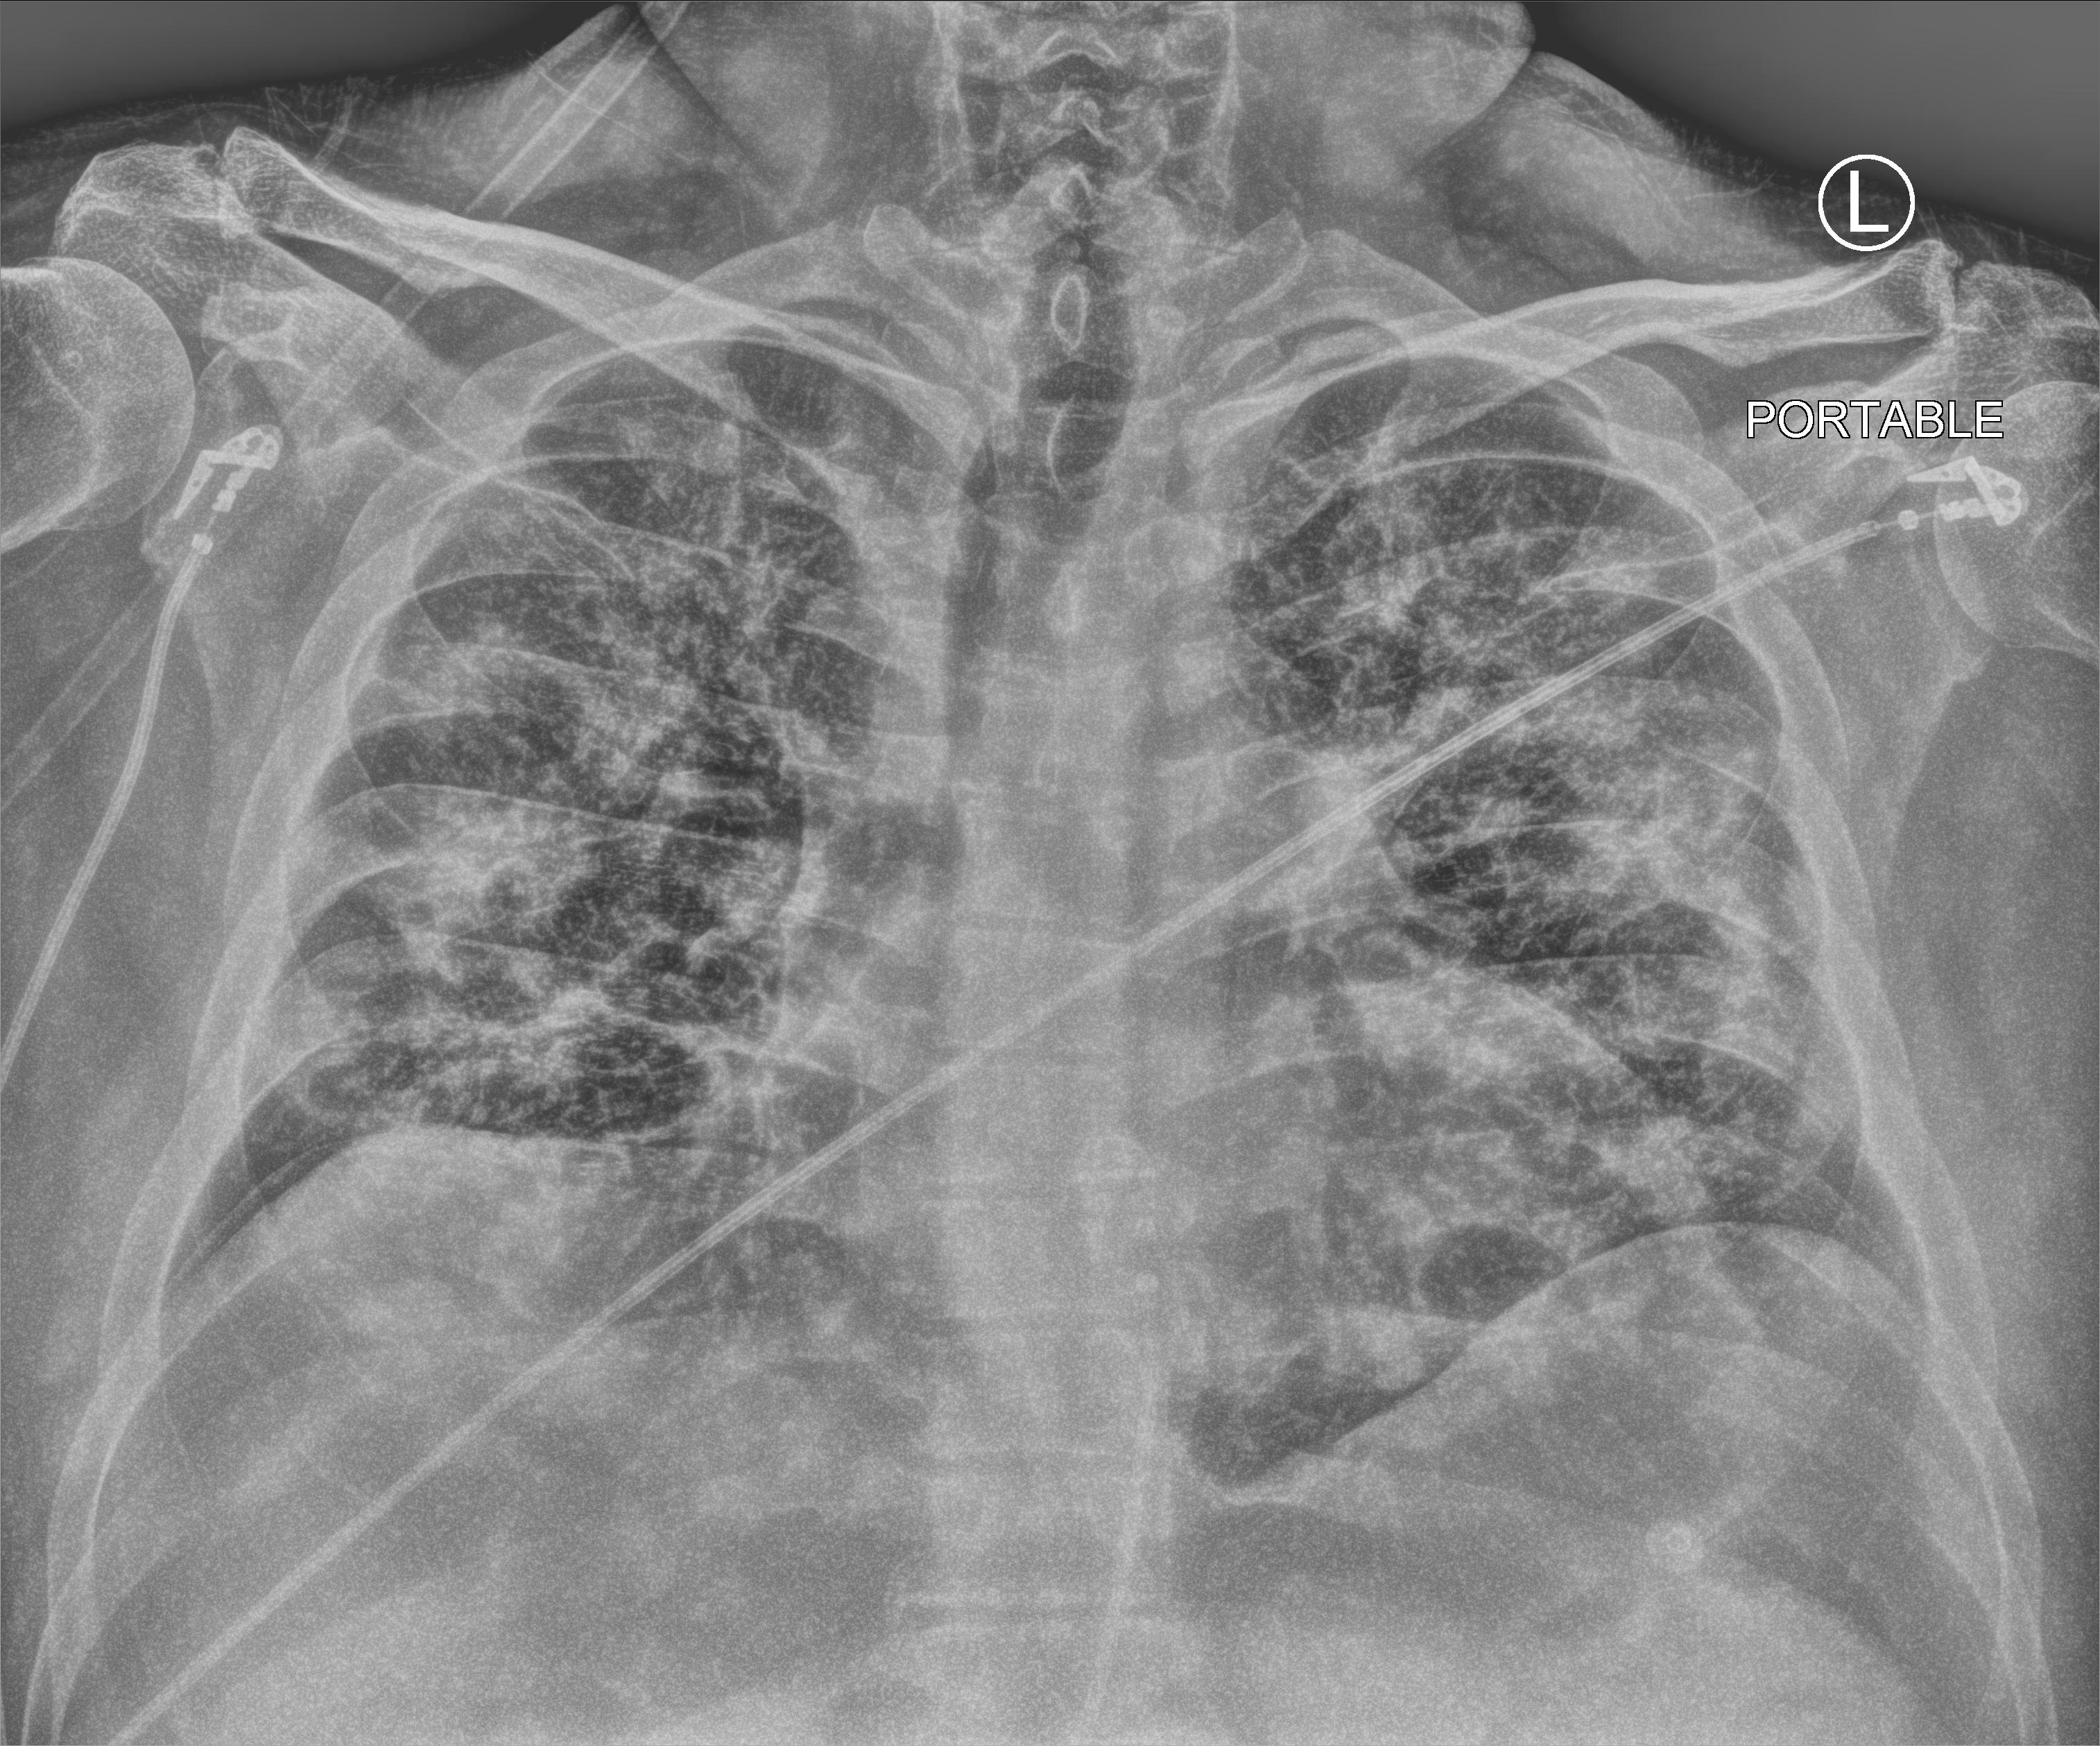
Portable chest radiograph, anteroposterior (AP) projection. Patient hospitalised with COVID-19; male, aged 18–59 years.
From the hospital-stay record, not from the radiograph (when in the stay this image was taken is not recorded): admitted to intensive care during this hospital stay: yes; diabetes (admission record): no; mechanically ventilated during this hospital stay: no.